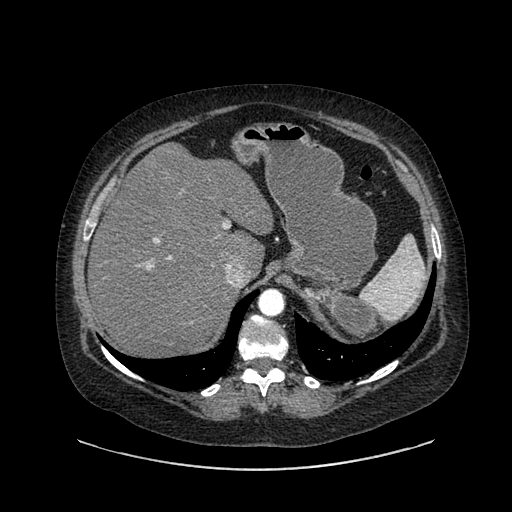
Contrast-enhanced abdominal CT, one axial slice. Position 635 of 769 along the scan axis. Reconstruction kernel SOFT. Intravenous contrast given. Soft-tissue window (W 400 / L 40 HU). 0.62 mm slice thickness. 512 × 512 image matrix, field of view 460 × 460 mm. Female patient, age 61 years. Case-level facts recorded for this patient, not image findings: diagnosis: adrenocortical carcinoma; tumour side: left adrenal; tumour size at pathology: 13 cm; Ki-67 index: 79 %; stage (as recorded): 2.
Outlined on this slice (semi-automatic segmentation, software-assisted and operator-edited):
- mass: bounding box [x1, y1, x2, y2] px = [308, 280, 374, 340]